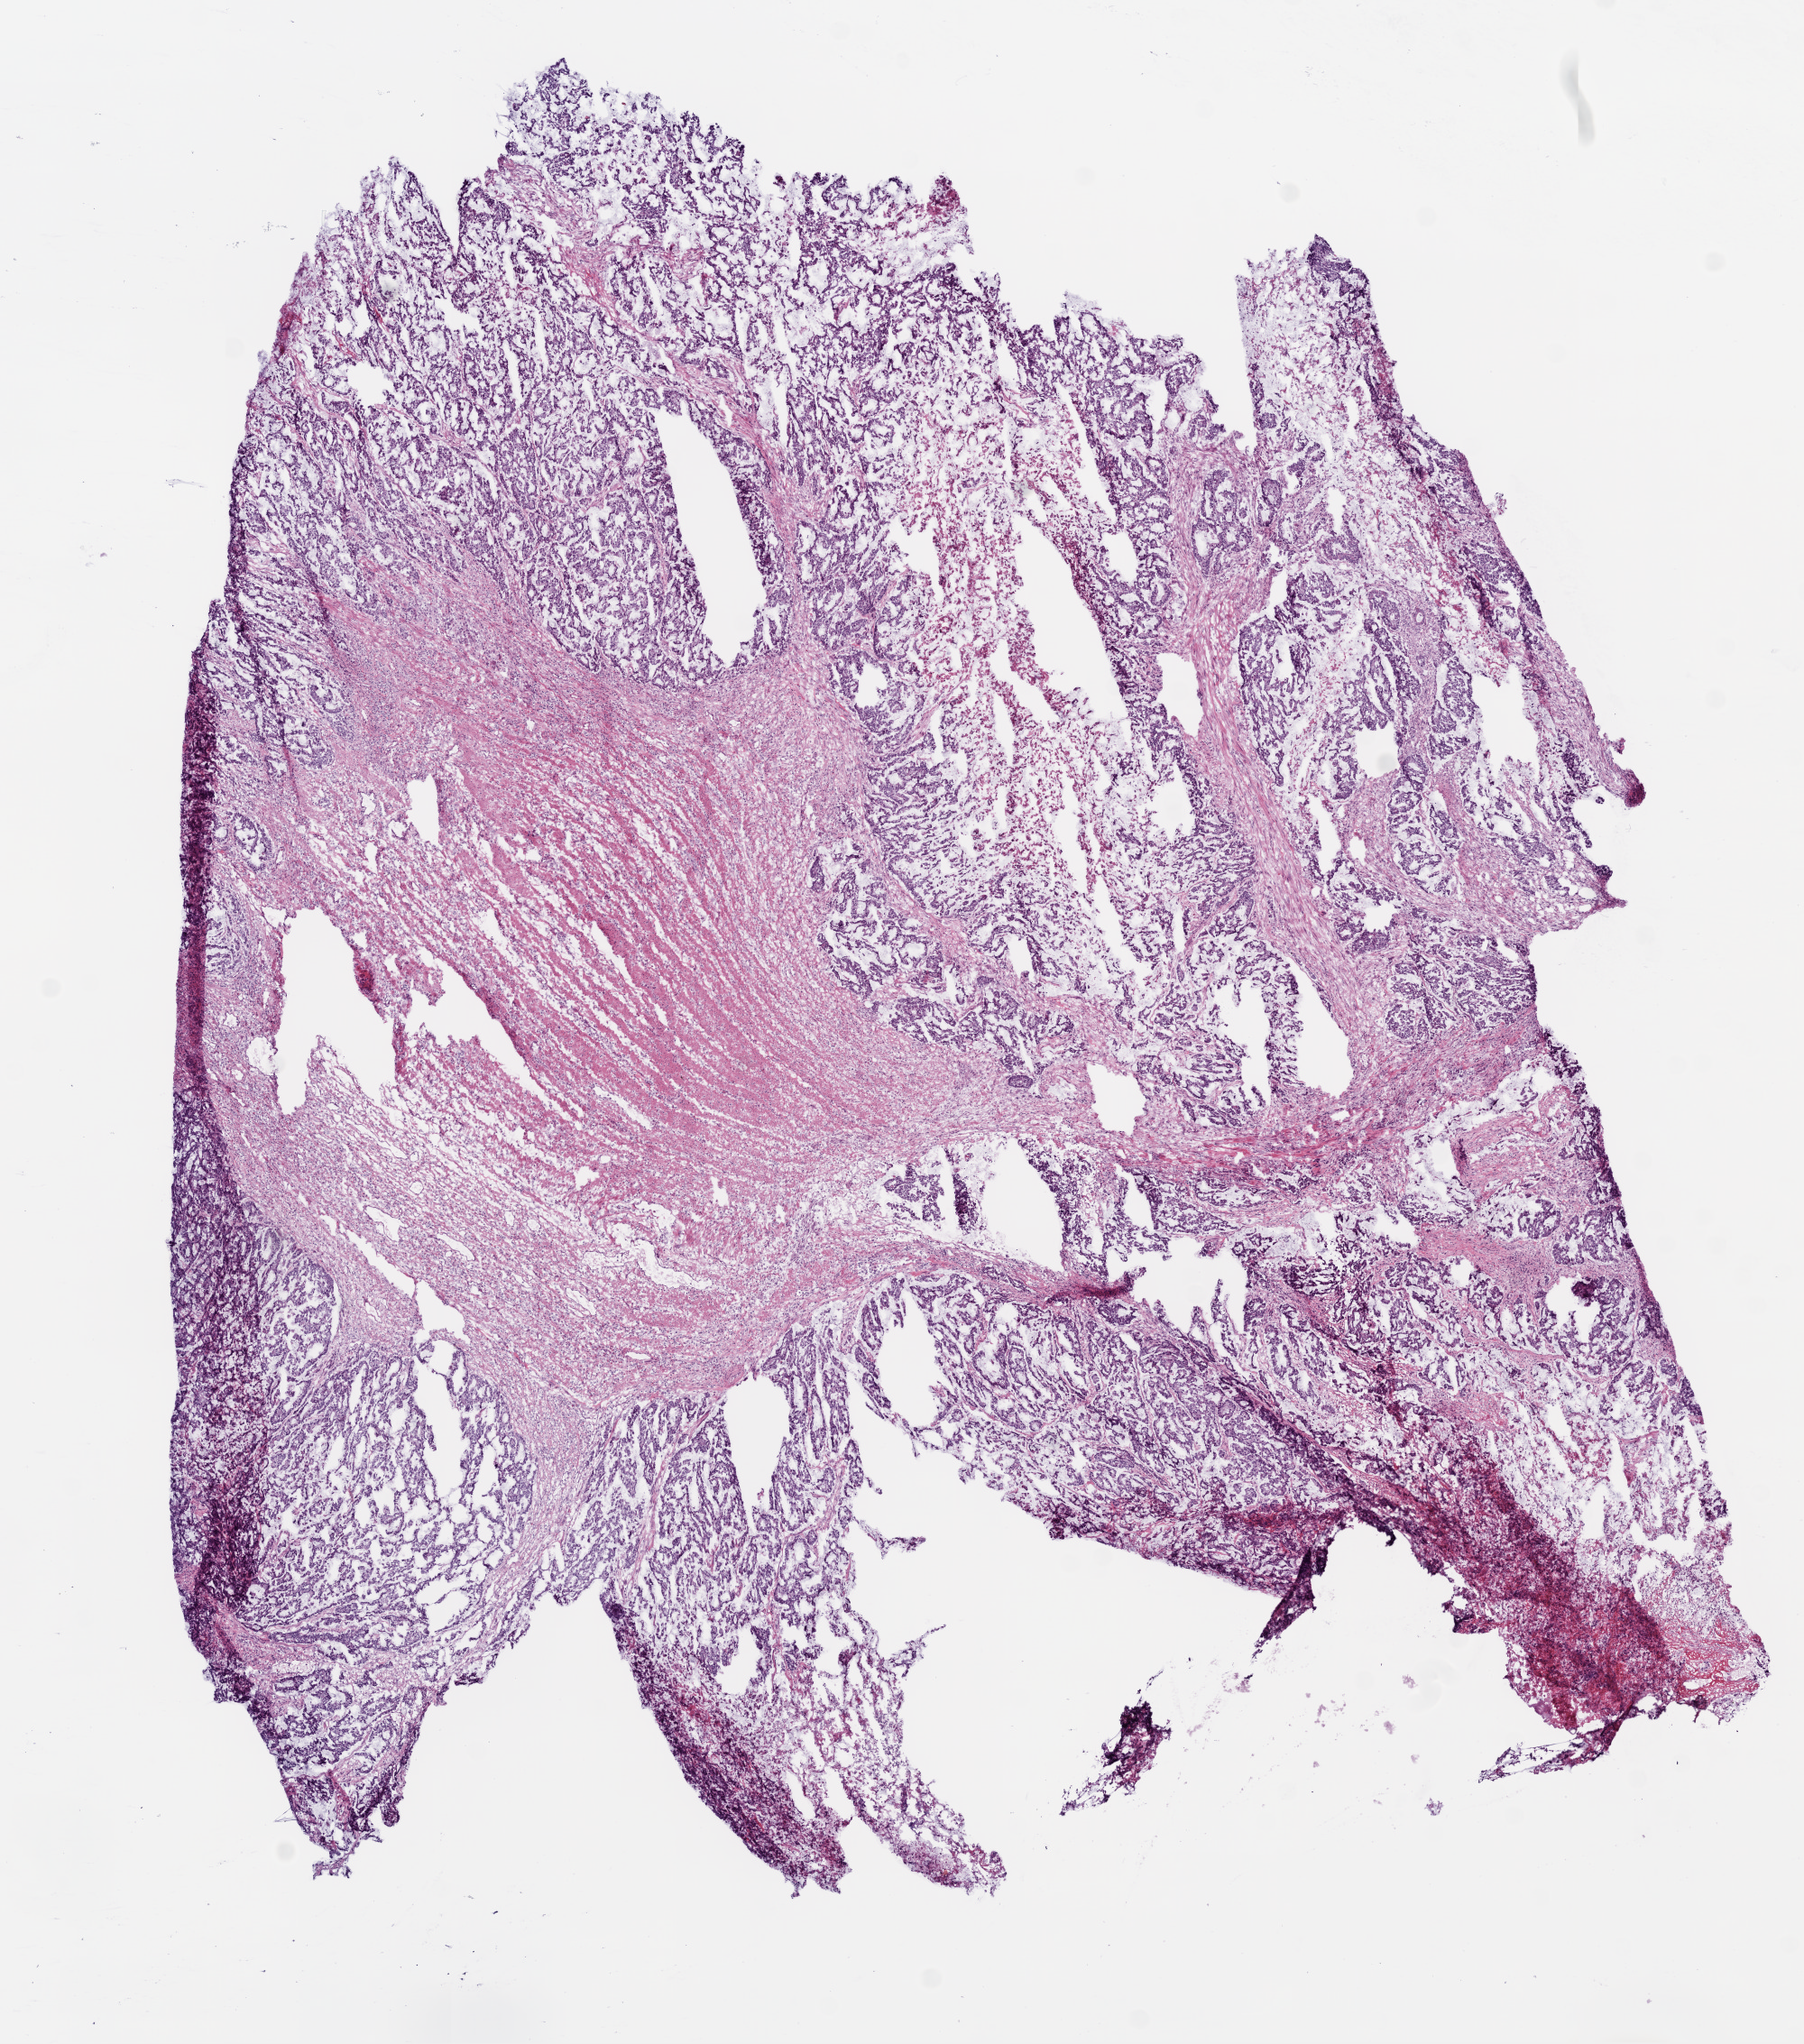
Digitized H&E-stained tissue section (whole slide), a low-resolution overview of the entire scanned area, about 8.0 x 9.1 mm. Frozen section from the bottom of the tissue portion. Rectum, primary tumour sample. Patient: female, age at initial diagnosis 83 years.
Diagnosis: Mucinous adenocarcinoma (unknown primary site).